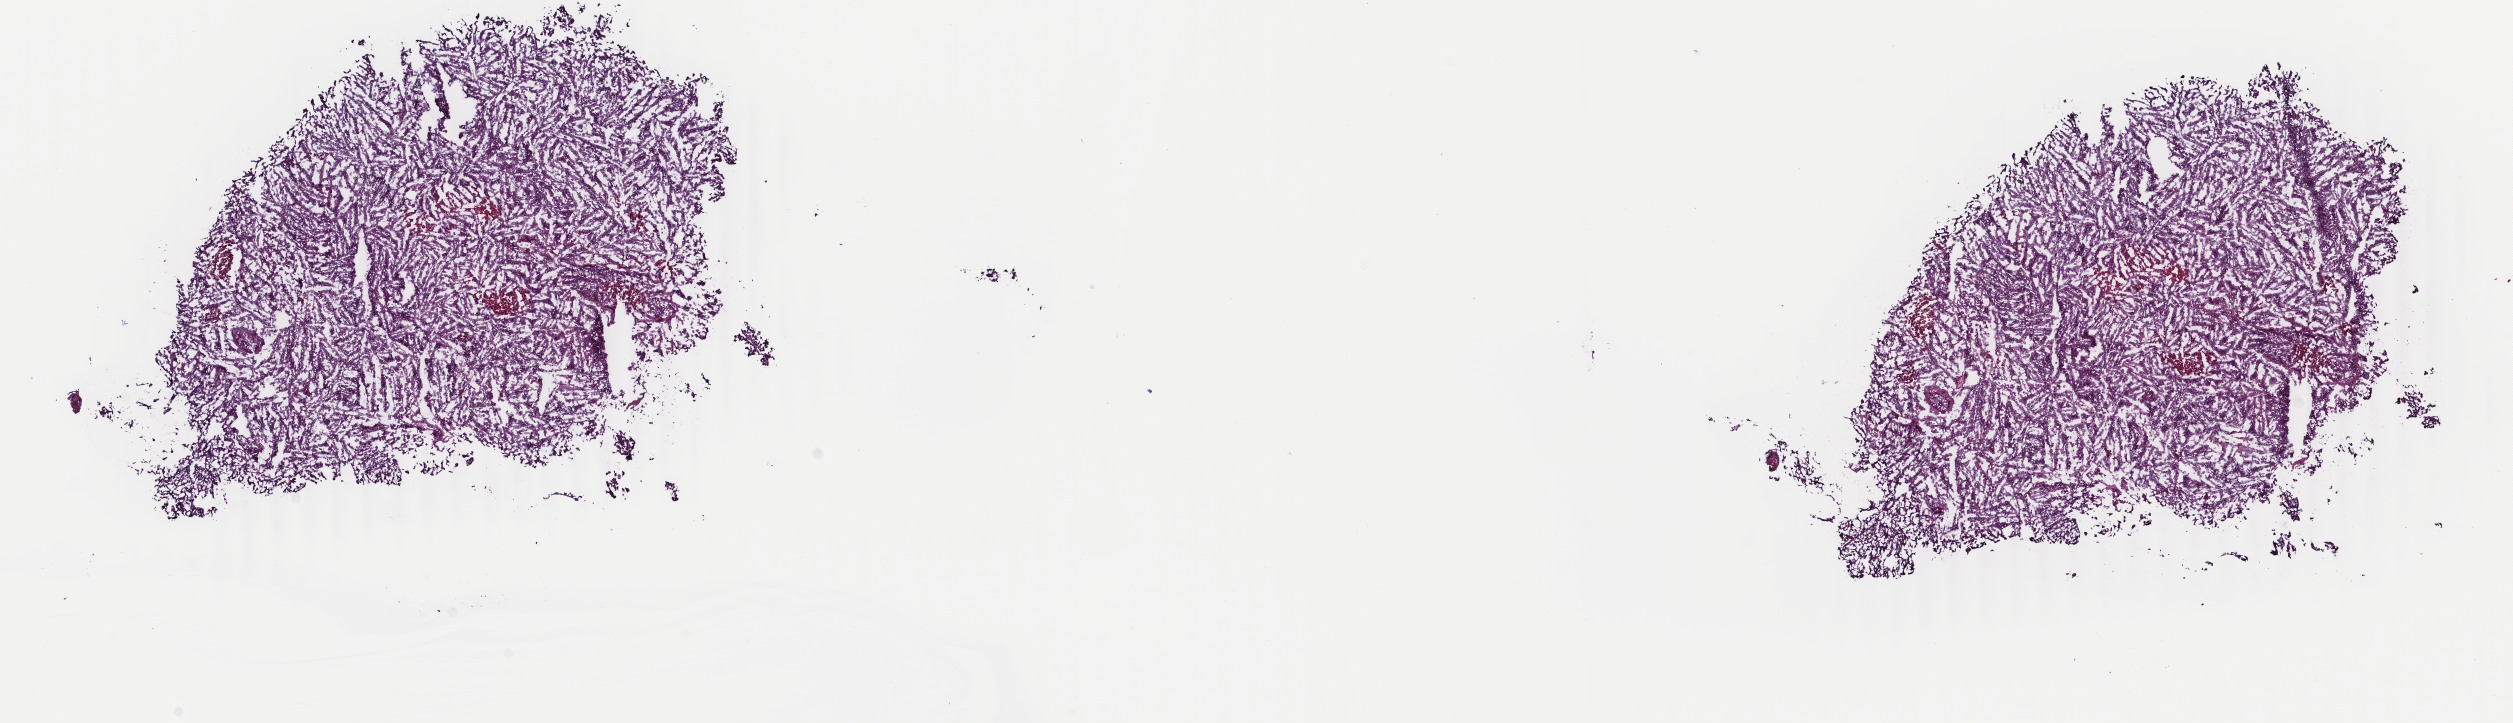
Digitized H&E-stained tissue section (whole slide), a low-resolution overview of the entire scanned area, about 20.0 x 5.8 mm (slide scanned at 40x), frozen section from the top of the tissue portion, adrenal cortex, primary tumour sample. Patient: female, age at initial diagnosis 53 years. Pathologist review of this section (percent, as recorded): tumour cells 90%, tumour nuclei 90%, normal cells 0%, stromal cells 1%, necrosis 9%. Inflammatory infiltration, as recorded: lymphocyte infiltration 0%, monocyte infiltration 0%, neutrophil infiltration 0%.
Laterality: right. Diagnosis: Adrenal cortical carcinoma (cortex of adrenal gland).